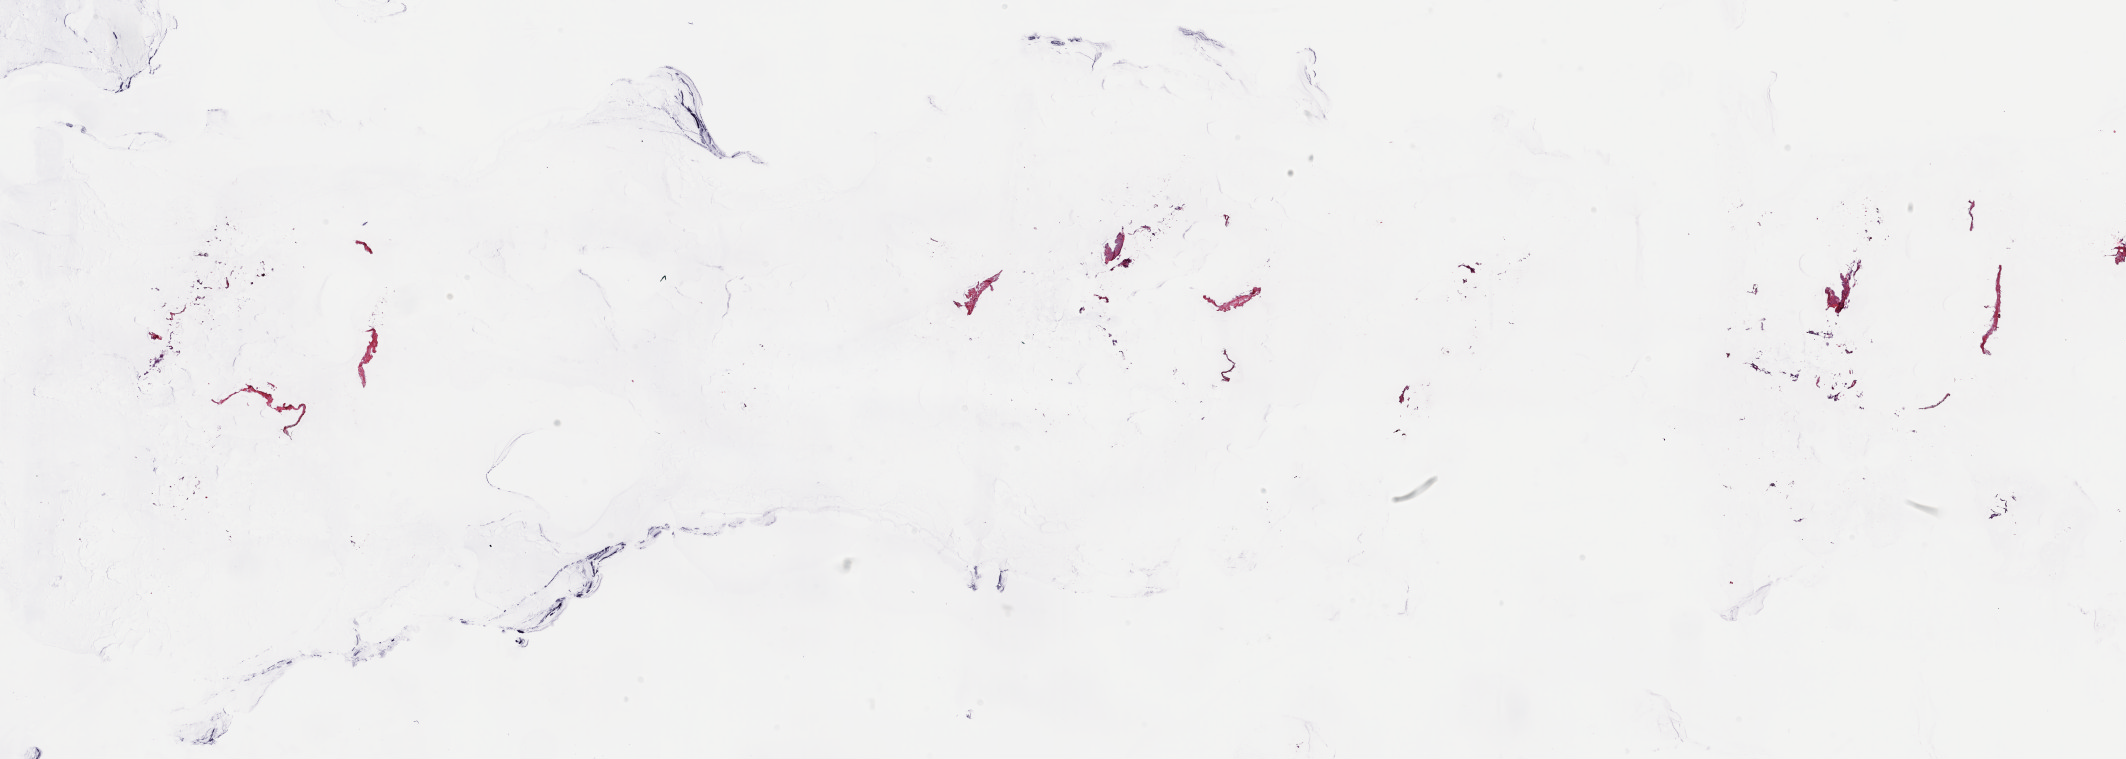
Digitized Hematoxylin and eosin (H&E) stained tissue section (whole slide) — shown as a low-resolution overview of the whole scanned area (about 33.7 x 12.0 mm), frozen section, sample: solid tissue normal (non-tumour tissue), breast. Female, age 54 years at initial diagnosis.
This section: solid tissue normal sample (biorepository sample class). Patient diagnosis: Infiltrating duct carcinoma, NOS.